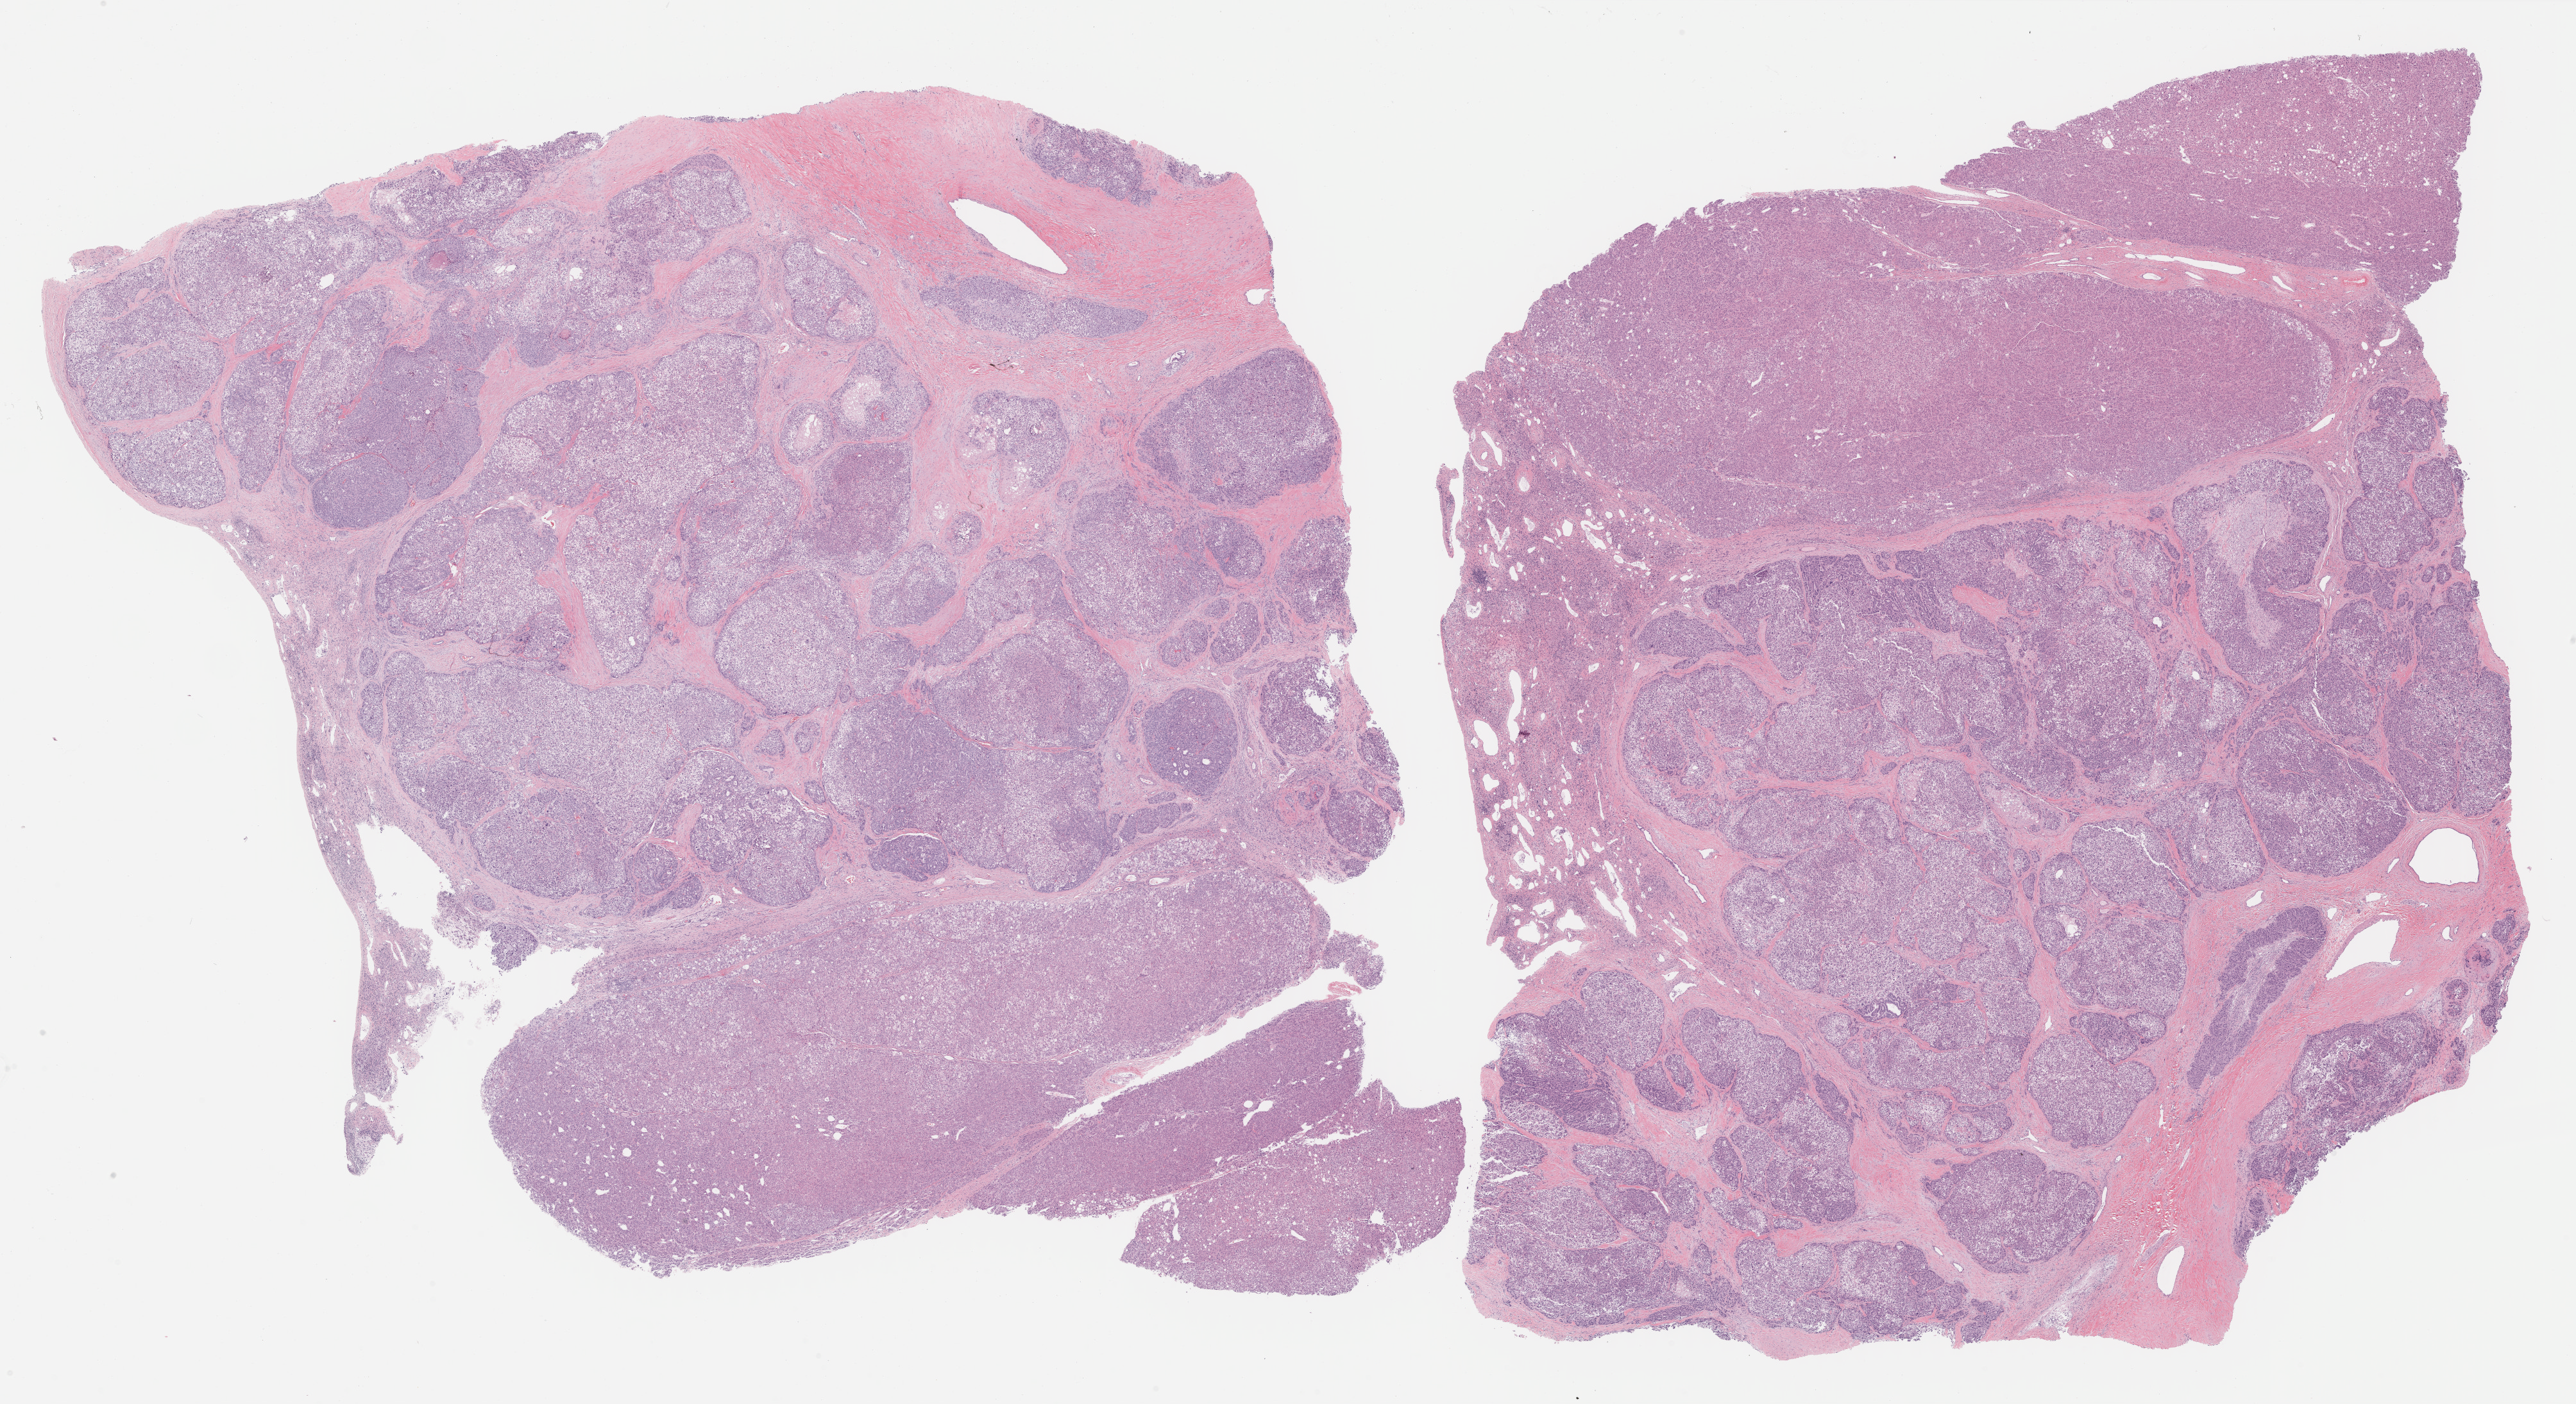
H&E-stained whole-slide image, a low-resolution overview of the entire scanned area, about 32.5 x 17.7 mm, formalin-fixed paraffin-embedded (FFPE) diagnostic section, sample: primary tumour, liver. Female, age 75 years at initial diagnosis. Histologic grade: G3 (poorly differentiated).
AJCC pathologic stage: IIIA (7th edition). Diagnosis: Hepatocellular carcinoma, NOS.